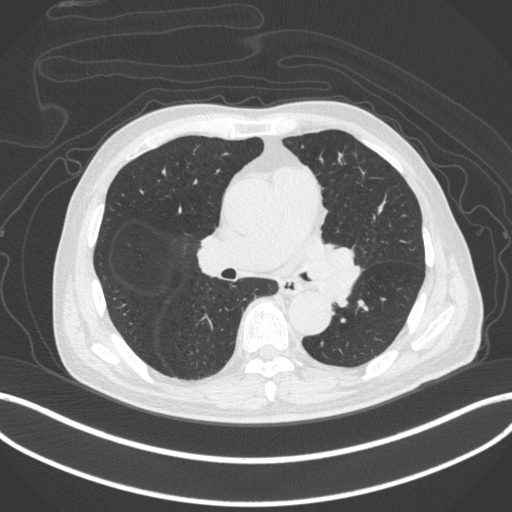
Chest CT, one axial slice. Slice 239 of 420 in the series (ordered by position). 120 kVp. Lung window (W 1500 / L -600 HU). 1 mm slice thickness. 512 × 512 image matrix, field of view 400 × 400 mm. Patient: male, 77 years. From the clinical record (not read from this slice): clinical TNM (as recorded): T3 N1 M0.
Structures marked on this image (rectangle marked by the reading radiologist):
- lung tumour (recorded histology: adenocarcinoma): box from (x=302, y=239) to (x=361, y=307) px